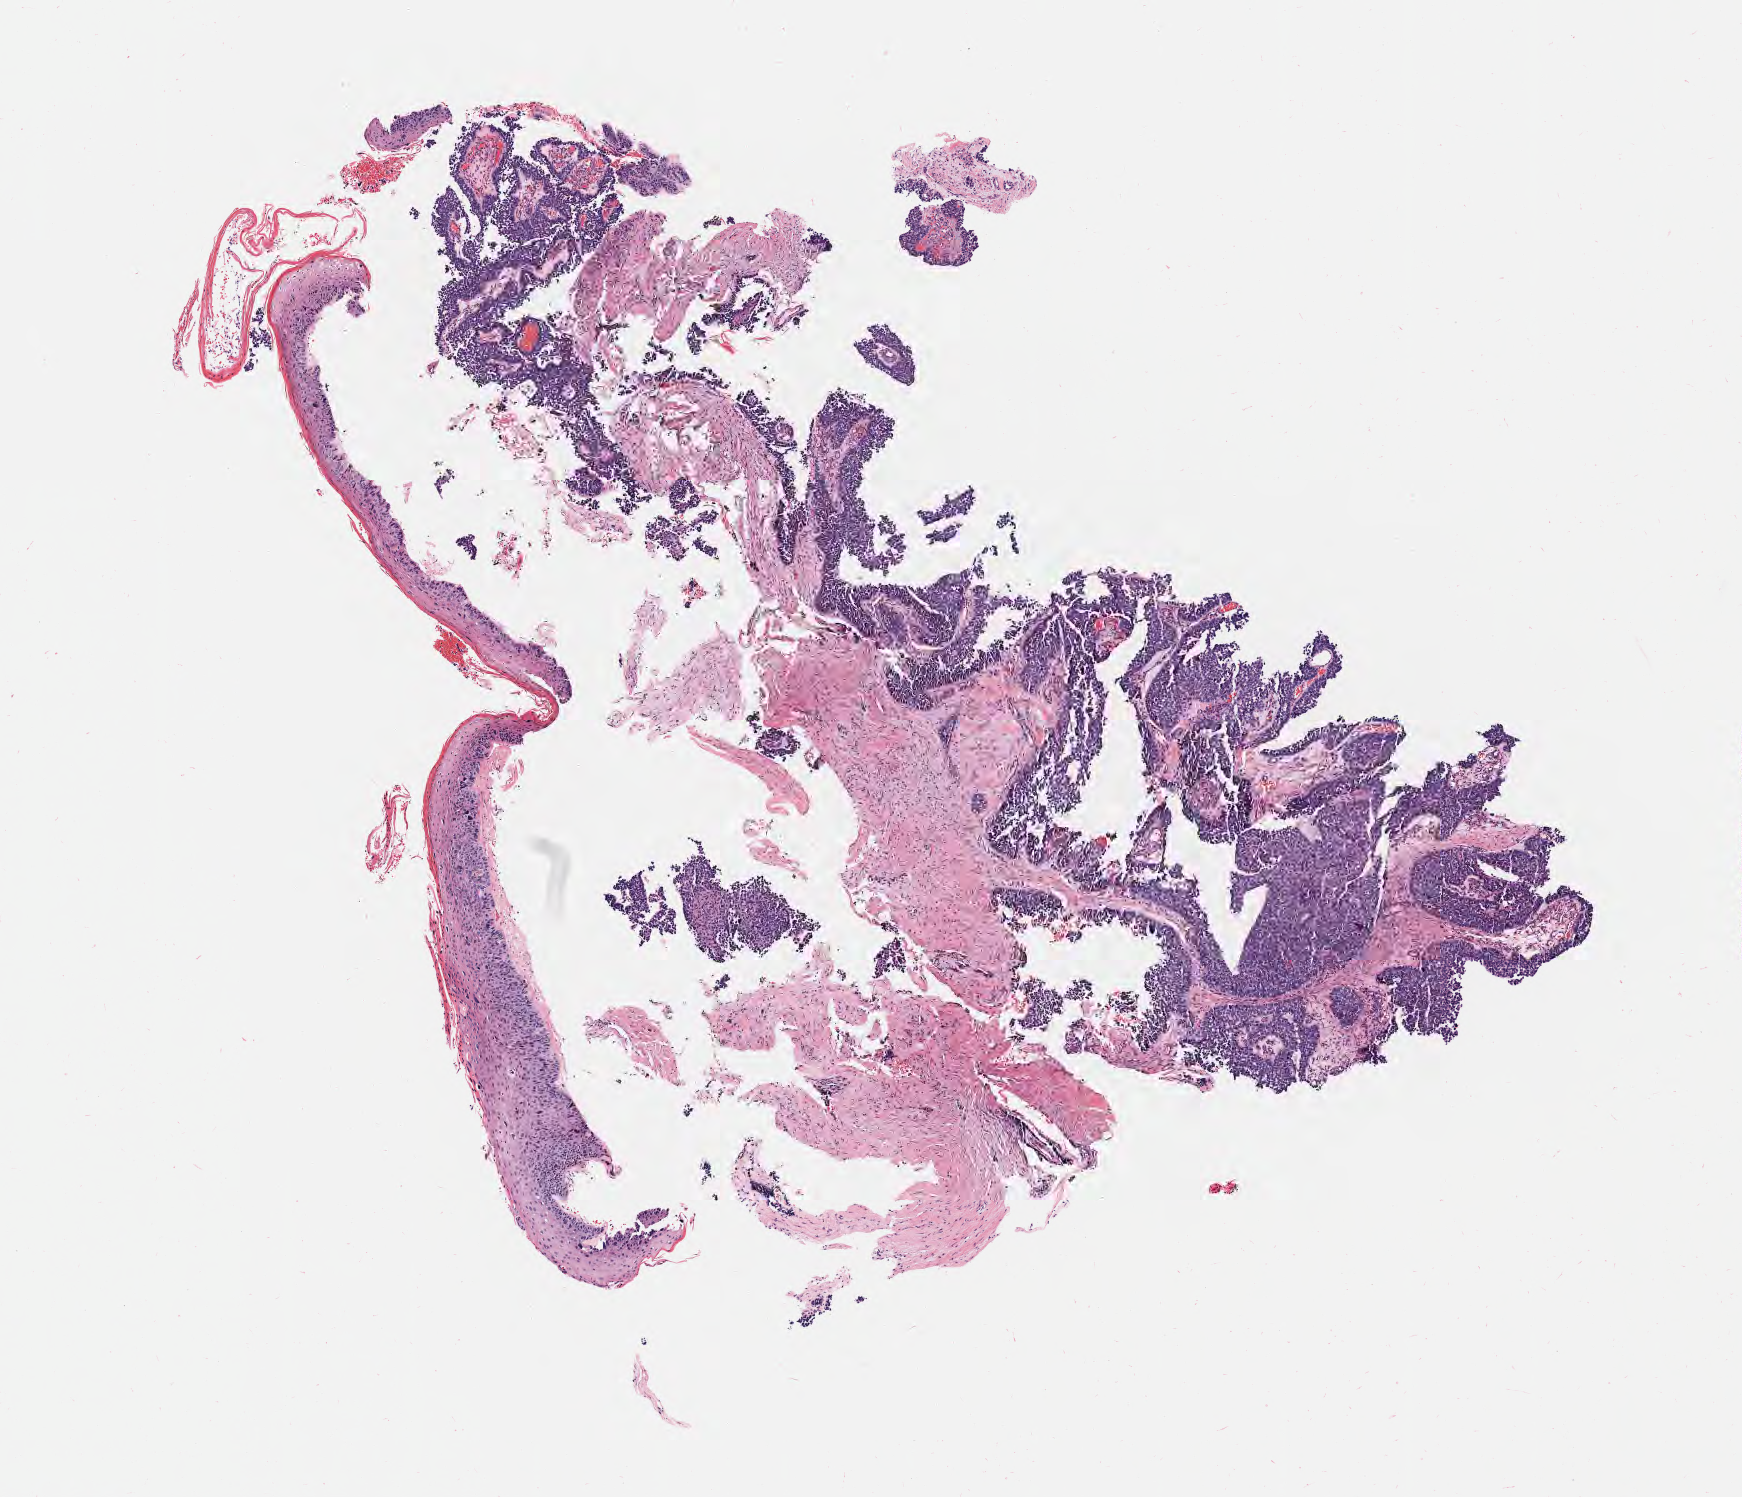
Haematoxylin and eosin whole-slide image — whole scanned area (about 7.0 x 6.1 mm) shown as a low-resolution overview. Tumor tissue. Anatomic site: cervix. Patient: female, 53 years old.
Diagnosis: Squamous cell carcinoma, large cell, nonkeratinizing, NOS.